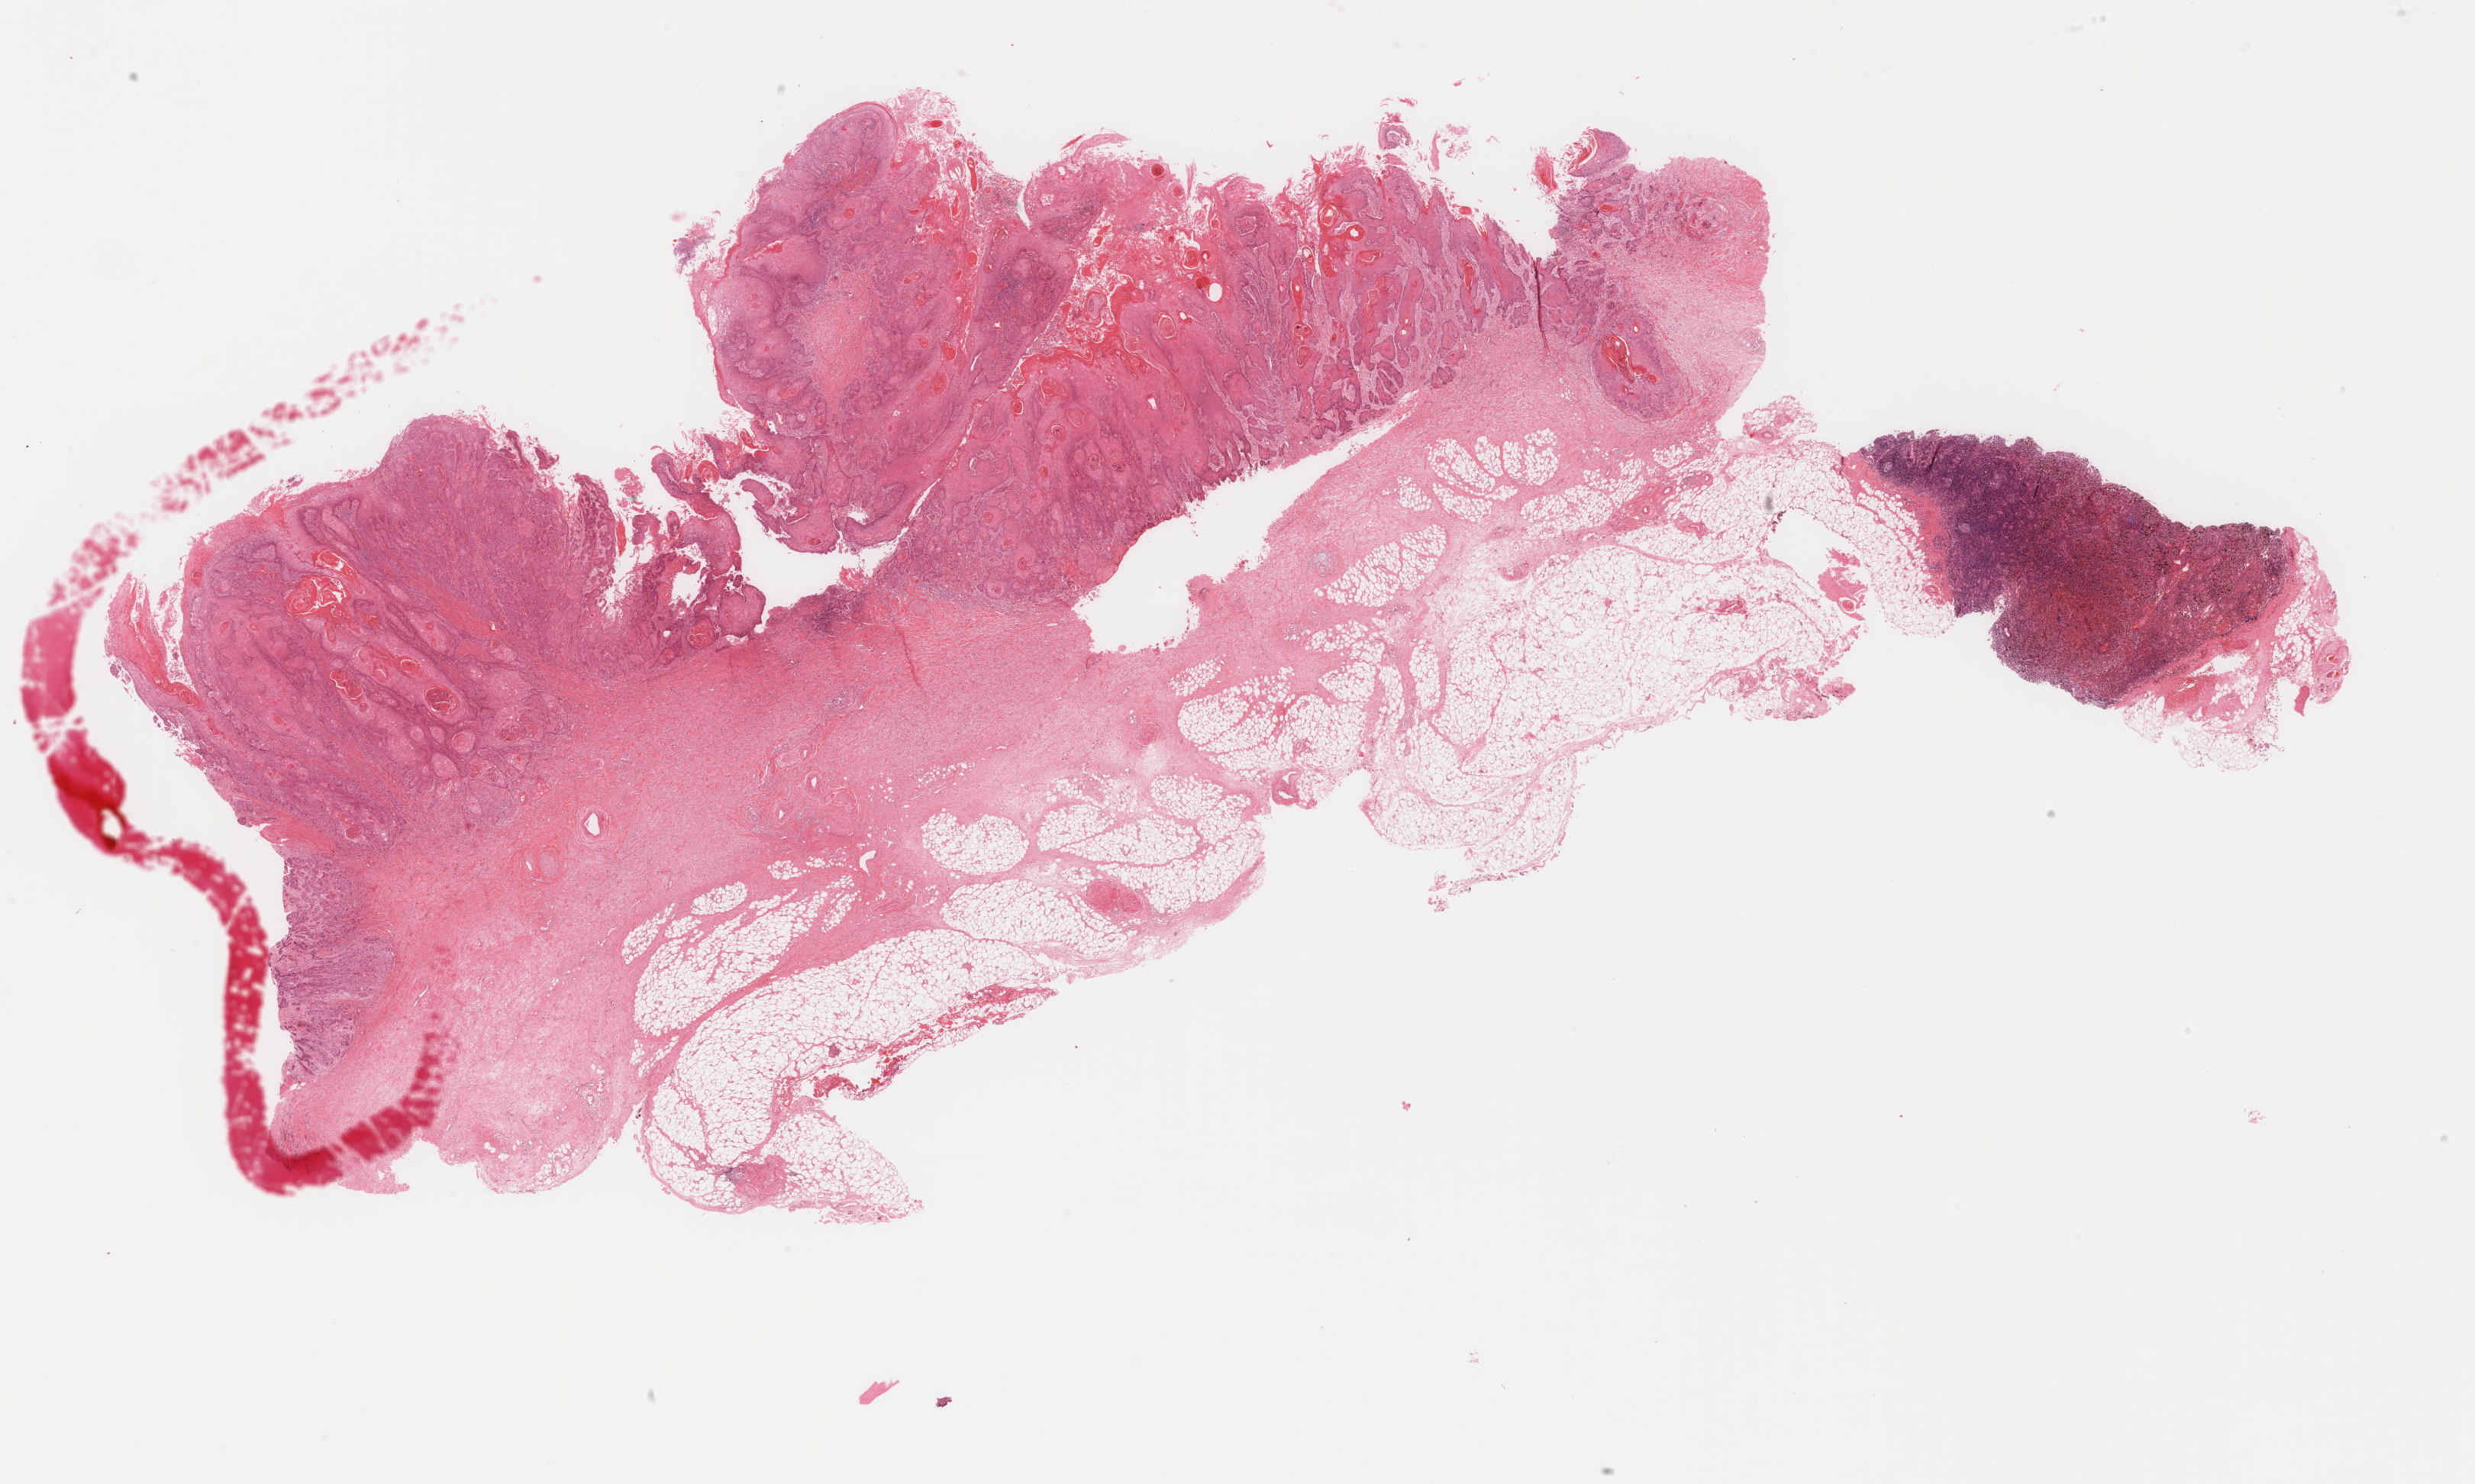
H&E whole-slide image — shown as a low-resolution overview of the whole scanned area (about 25.7 x 15.4 mm, slide scanned at 40x). Formalin-fixed paraffin-embedded (FFPE) diagnostic section. Primary tumour sample from the esophagus. Male, age 56 years at initial diagnosis. Histologic grade: G2 (moderately differentiated).
AJCC pathologic stage: IIA (7th edition). TNM: T3 N0 M0. Histologic diagnosis: Squamous cell carcinoma, keratinizing, NOS (thoracic esophagus). Lymph nodes positive (case pathology): 0 of 17 examined.